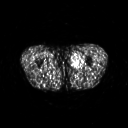
FDG PET of an extremity soft-tissue mass (from a PET/CT study), one axial slice; 3.27 mm slice thickness; 128 × 128 image matrix, field of view 500 × 500 mm. Male patient, age 29 years. From the clinical record (not read from this slice): histological type: mixoid liposarcoma; grade: low; site of the primary tumour: left thigh.
Annotated regions visible in this slice (expert contour drawn on MRI and transferred to this co-registered scan by the dataset authors):
- gross tumour volume (mass): box from (x=70, y=53) to (x=83, y=68) px